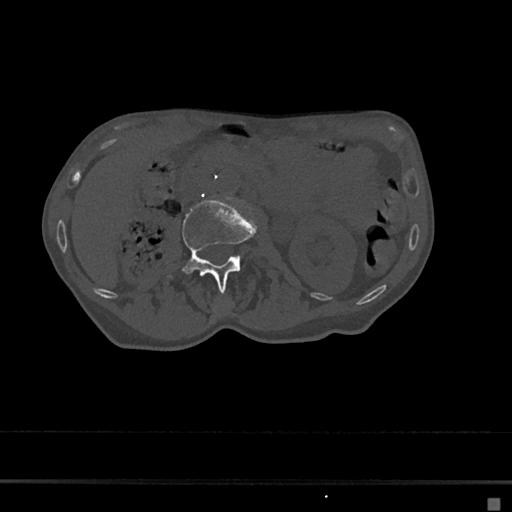
CT including the spine, one axial slice; slice 10 of 797 in the series (ordered by position); reconstruction kernel Br40s/3; 120 kVp; bone window (W 1800 / L 400 HU); 512 × 512 image matrix, field of view 360 × 360 mm. Patient: female, 68 years. From the clinical record (not read from this slice): primary cancer: renal.
Outlined on this slice (semi-automatically segmented with operator editing):
- L2 vertebra: bounding box [x1, y1, x2, y2] px = [174, 199, 258, 291]